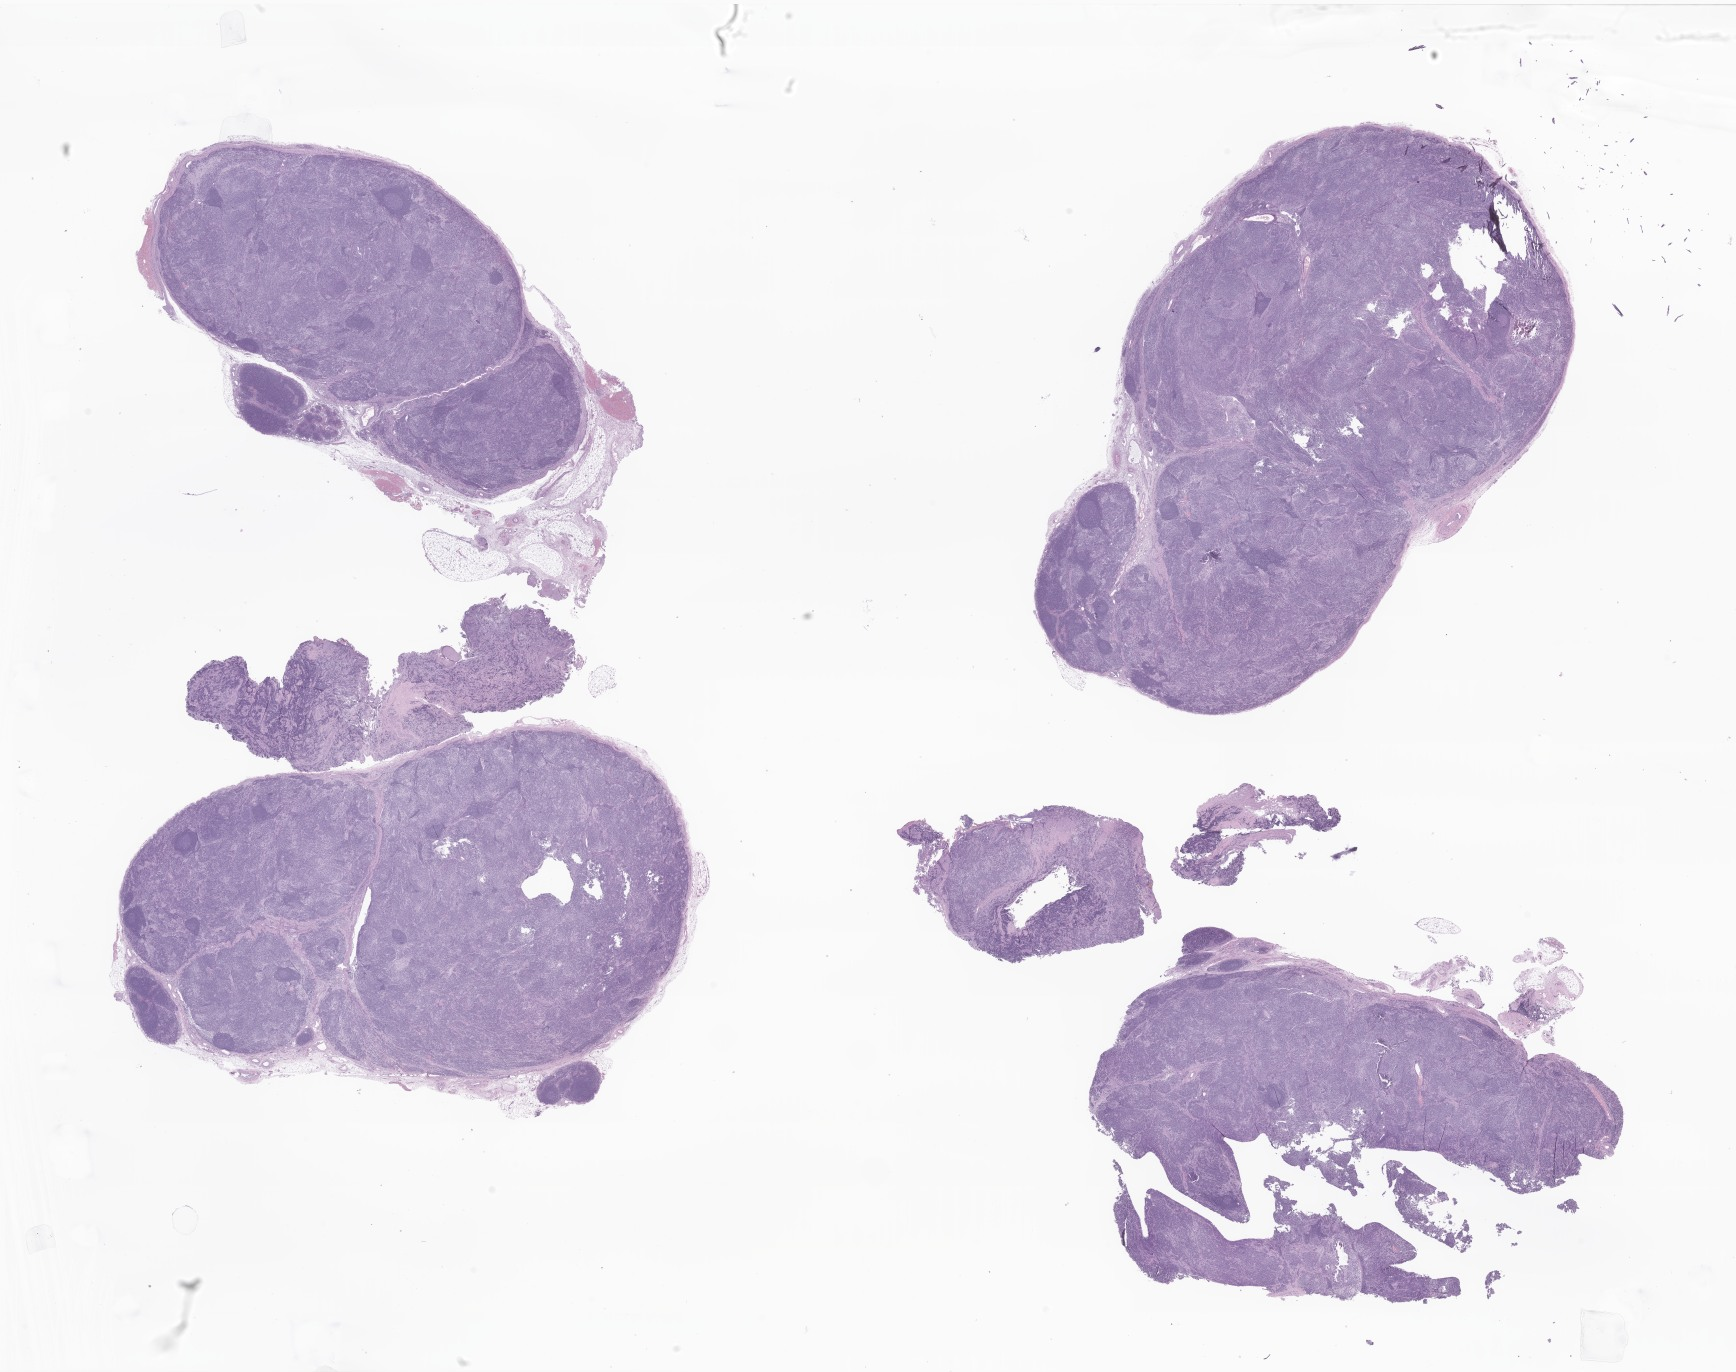
H&E whole-slide image of tumor tissue from the mediastinum — shown as a low-resolution overview of the whole scanned area (about 29.3 x 23.1 mm). Formalin-fixed paraffin-embedded section. Patient female; age 496 days (about 1.4 years).
Diagnosis (ICD-O-3 morphology term): Neuroblastoma, NOS.